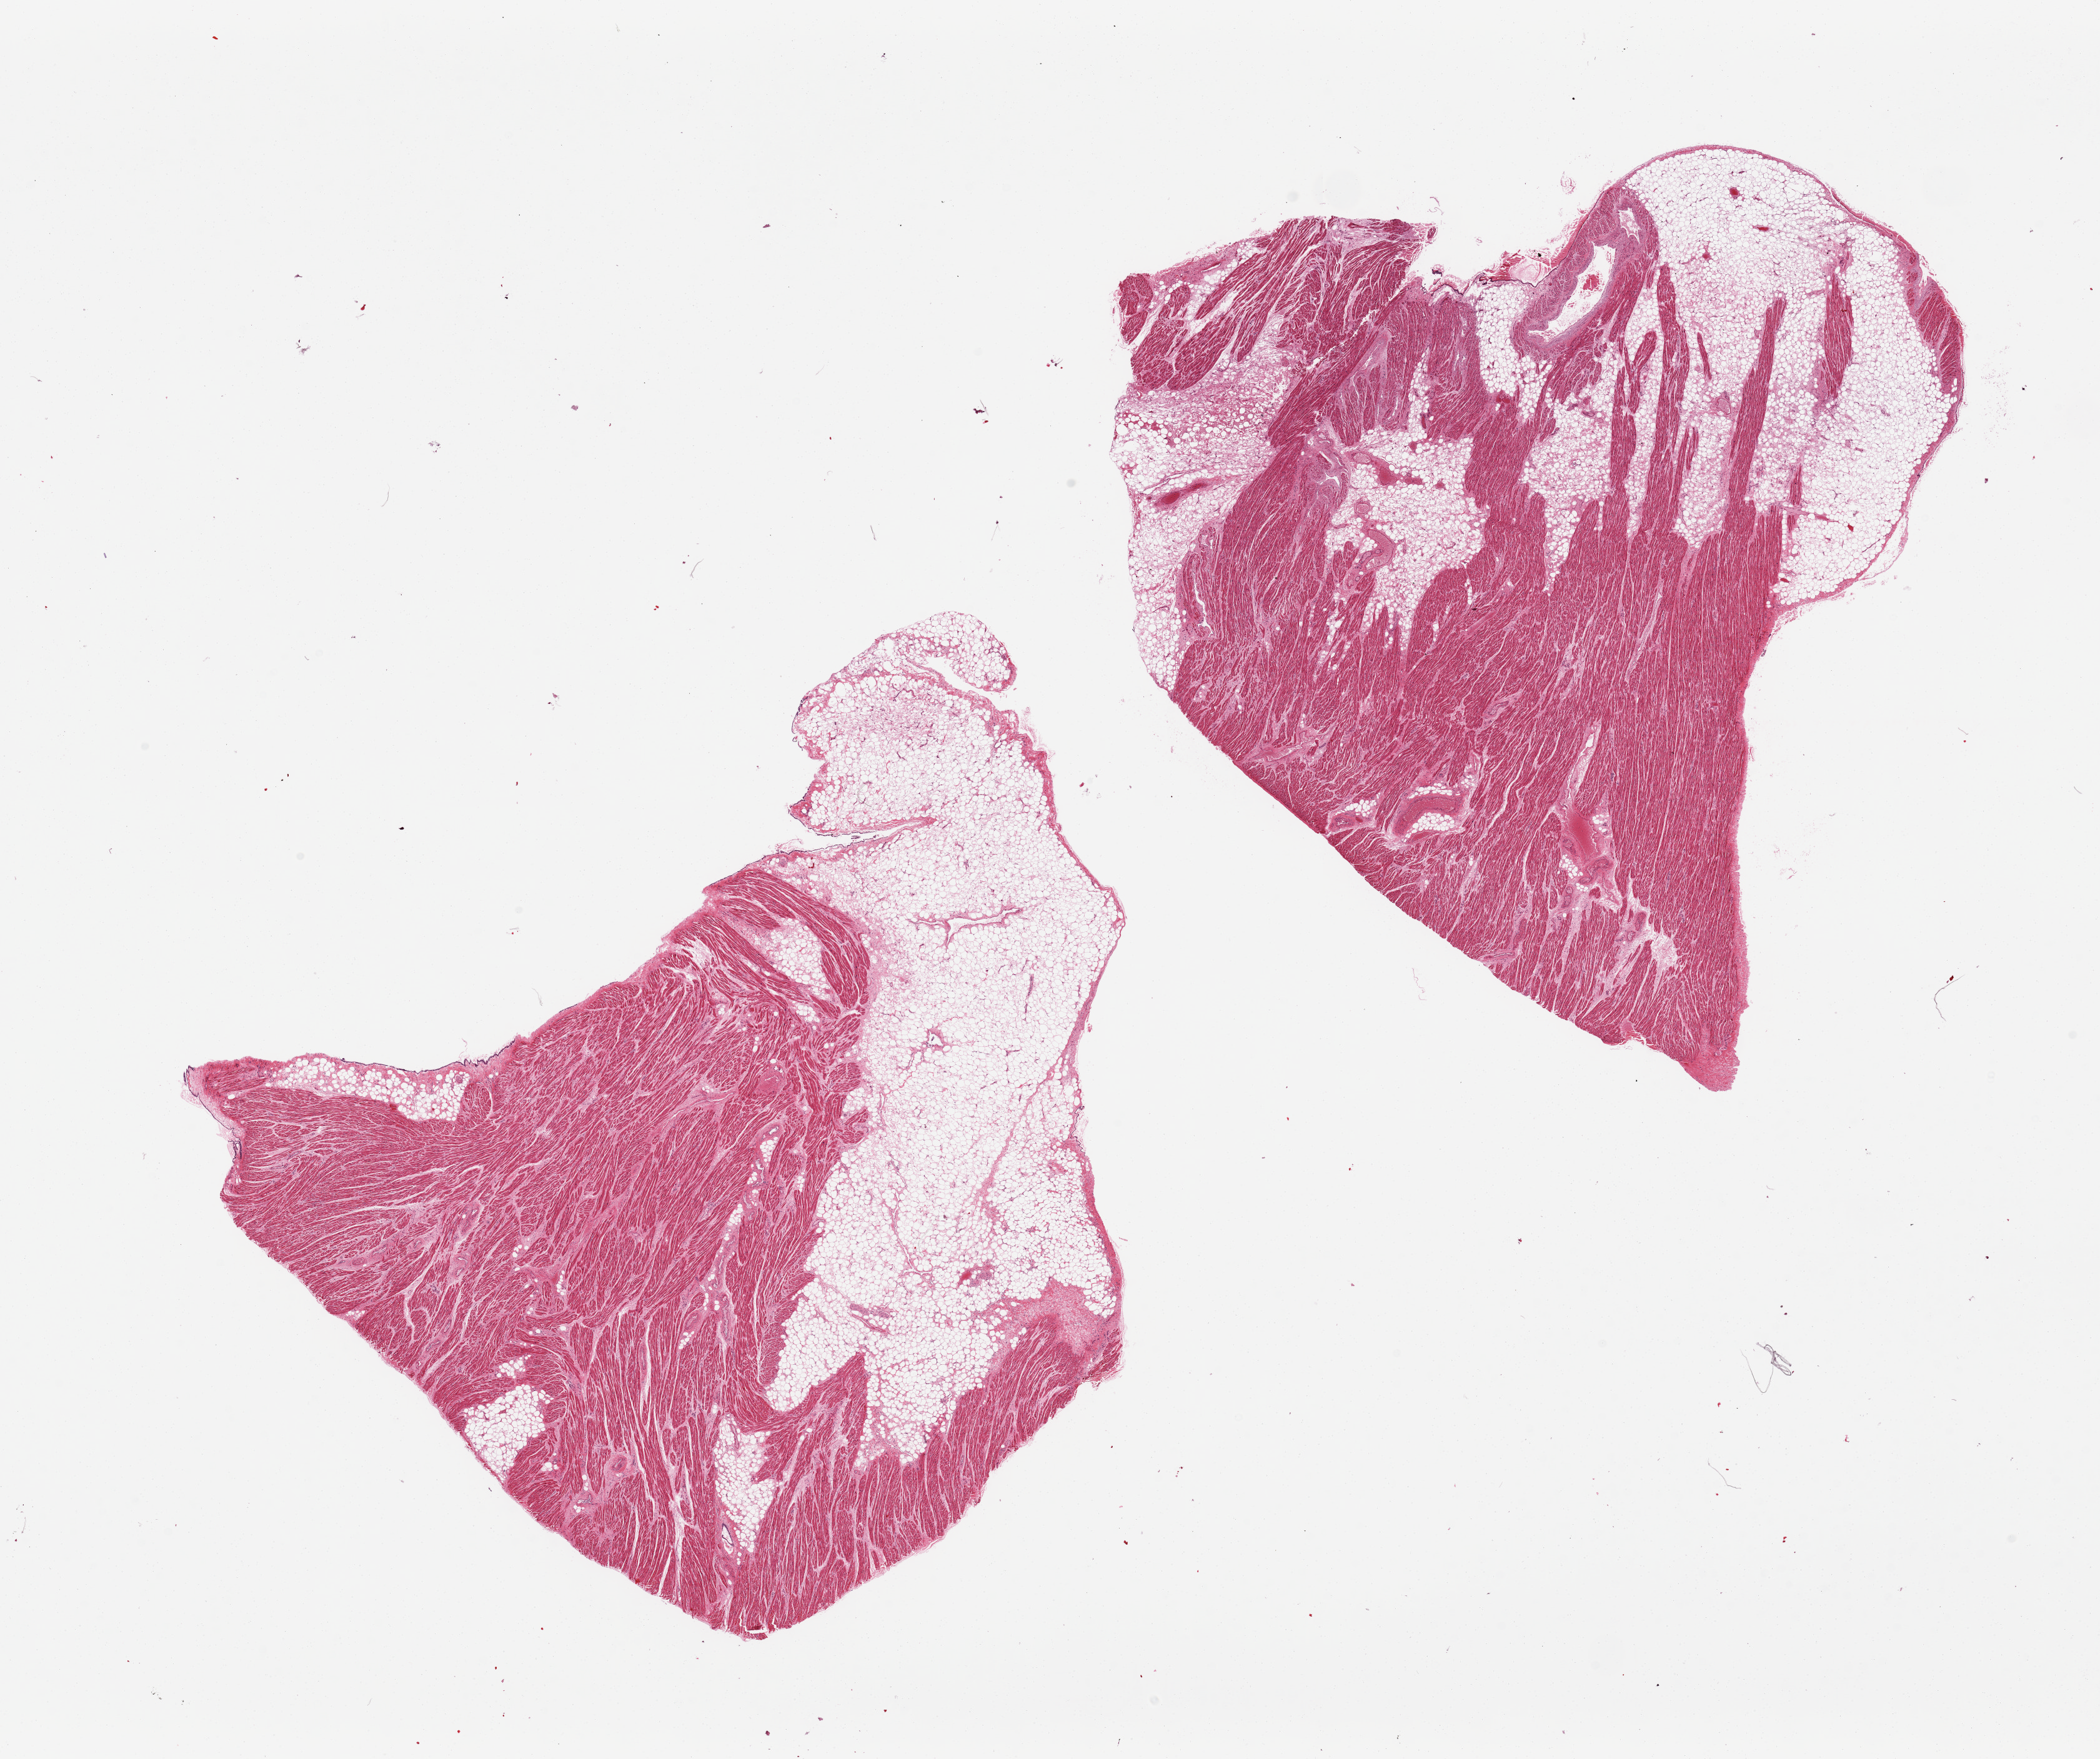
H&E whole-slide image — whole scanned area (about 26.6 x 22.3 mm, slide scanned at 20x) shown as a low-resolution overview; PAXgene-fixed paraffin-embedded (PFPE) section; section of auricular appendage (target tissue); tissue donor sample. Donor: male.
Reviewer comment on this tissue sample: 2 pieces, both ~40% fat, myocyte hypertrophy.